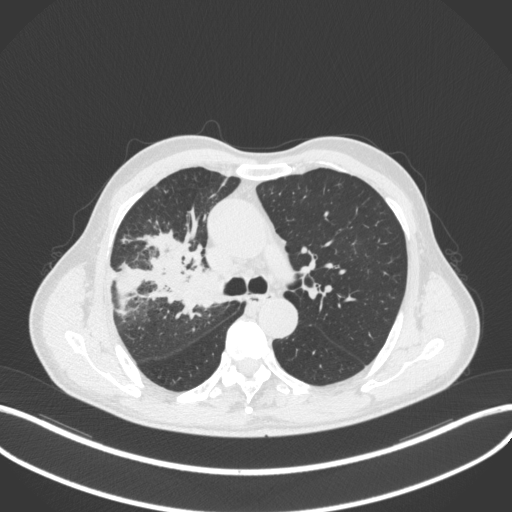
Chest CT, one axial slice; position 323 of 490 along the scan axis; reconstruction kernel B31f; lung window (W 1500 / L -600 HU); 1 mm slice thickness; 512 × 512 image matrix. Patient: male, 69 years. From the clinical record (not read from this slice): clinical TNM (as recorded): T2a N0 M0.
Structures marked on this image (rectangle marked by the reading radiologist):
- lung tumour (recorded histology: adenocarcinoma): bounding box (x1, y1, x2, y2) in pixels: (172, 270, 217, 311)